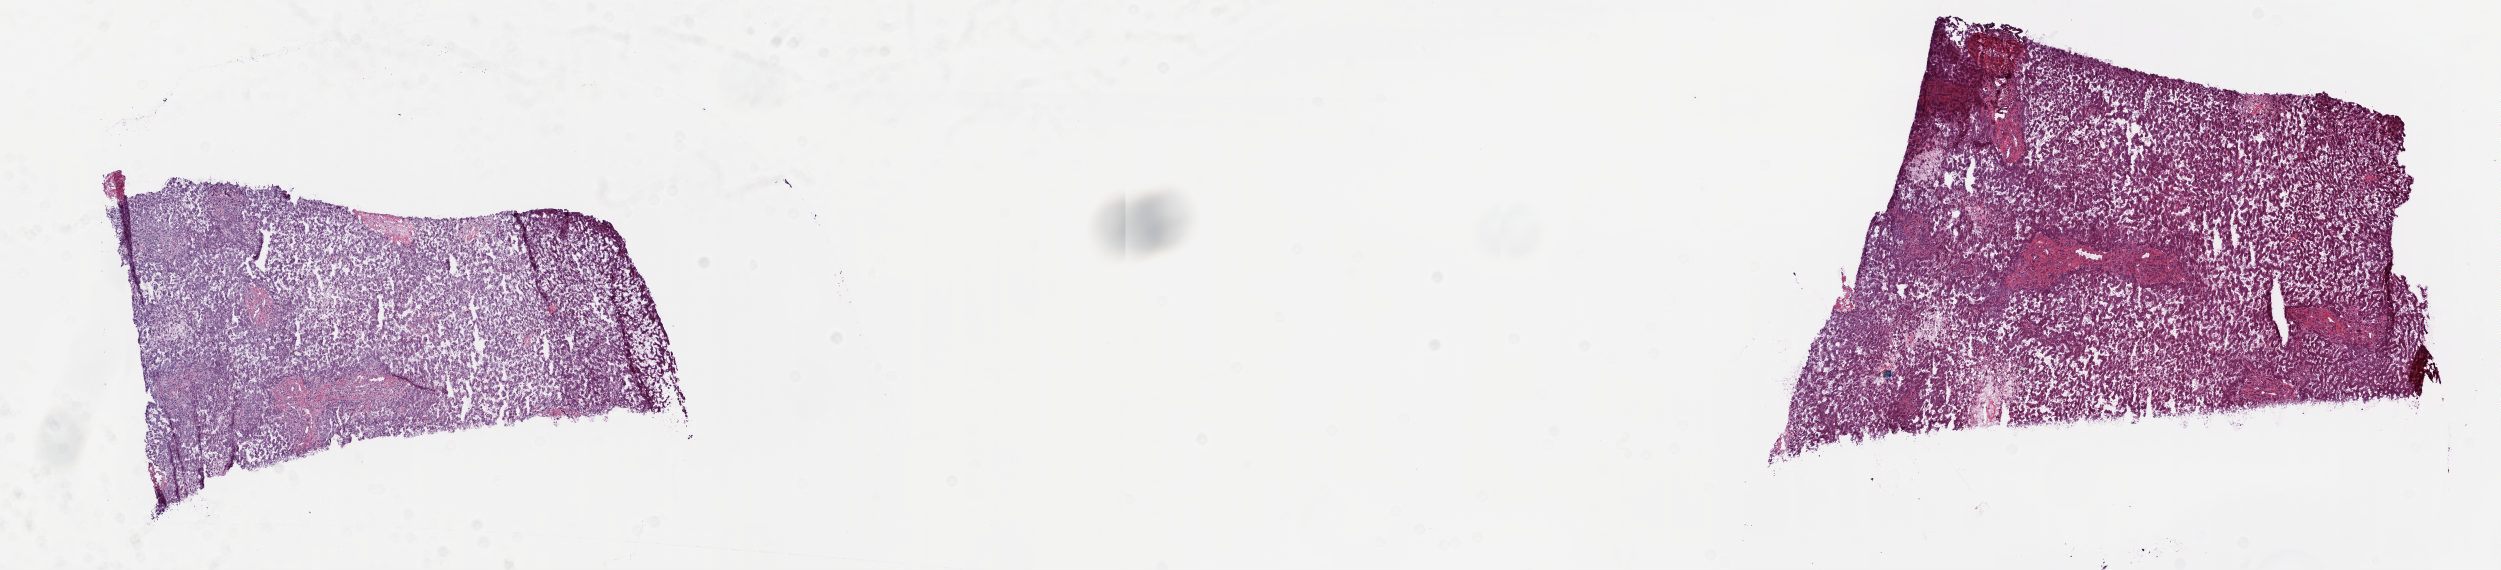
Digitized H&E-stained tissue section (whole slide) — shown as a low-resolution overview of the whole scanned area (about 19.8 x 4.5 mm, slide scanned at 20x). Frozen section. Sample: solid tissue normal (non-tumour tissue), bile duct. Patient: female, age at initial diagnosis 29 years. Slide review estimates, as recorded: tumour cells 0%, tumour nuclei 0%, normal cells 90%, stromal cells 10%, necrosis 0%. Infiltration values recorded for this section: lymphocyte infiltration 6%, monocyte infiltration 0%, neutrophil infiltration 0%.
This section: solid tissue normal sample (biorepository sample class). Patient diagnosis: Cholangiocarcinoma (intrahepatic bile duct).